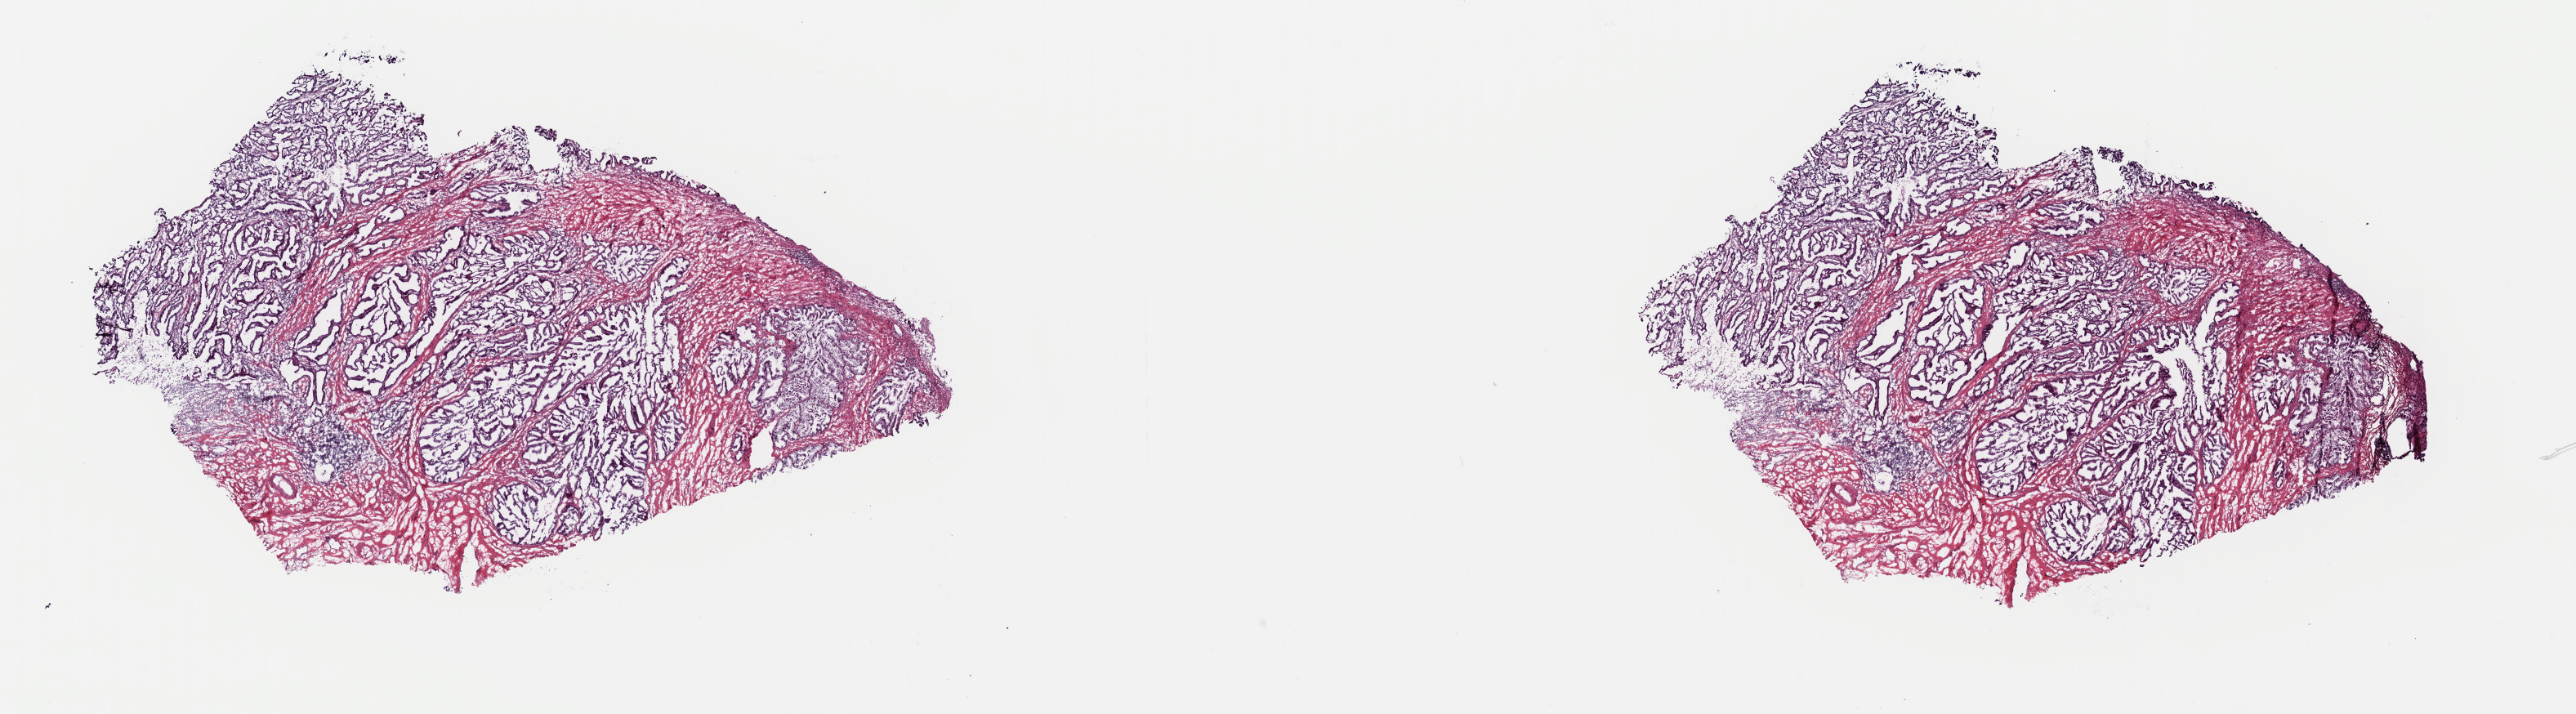
H&E whole-slide image, low-resolution overview of the scanned area, about 24.9 x 6.9 mm. Frozen section from the top of the tissue portion. Cervix, primary tumour sample. Female, age 64 years at initial diagnosis. Histologic grade: G2 (moderately differentiated). Pathologist review of this section (percent, as recorded): tumour cells 70%, tumour nuclei 60%, normal cells 30%, stromal cells 0%, necrosis 0%. Inflammatory infiltration, as recorded: lymphocyte infiltration 0%, monocyte infiltration 0%, neutrophil infiltration 0%.
Lymph nodes positive (case pathology): 0 of 16 examined. FIGO stage: IB1. Diagnosis: Adenocarcinoma, endocervical type (cervix uteri).